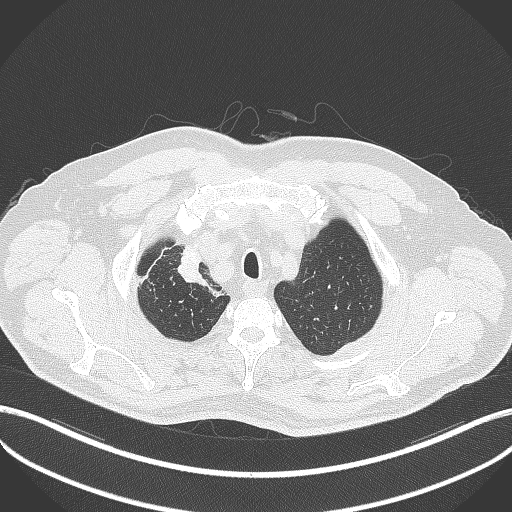
Chest CT, one axial slice; slice 336 of 411 in the series (ordered by position); lung window (W 1500 / L -600 HU); 1 mm slice thickness; 512 × 512 image matrix. Patient: male, 60 years. Case-level facts recorded for this patient, not image findings: clinical TNM (as recorded): T1b N1 M0.
Outlined on this slice (rectangle marked by the reading radiologist):
- lung tumour (recorded histology: squamous cell carcinoma): bounding box [x1, y1, x2, y2] px = [178, 249, 209, 288]